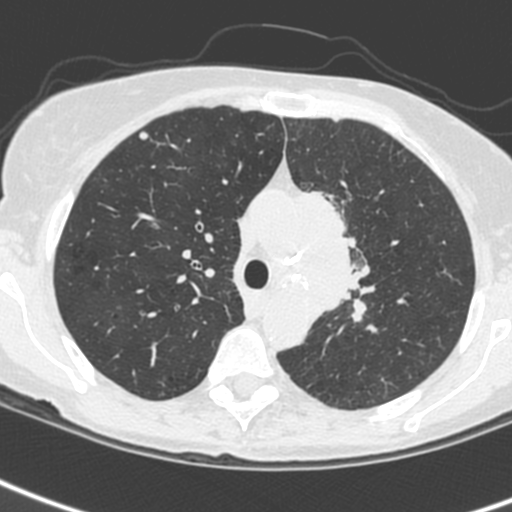
Low-dose screening chest CT, one axial slice. Slice 176 of 242 in the series (ordered by position). 120 kVp. Lung window (W 1500 / L -600 HU). 1.3 mm slice thickness. 512 × 512 image matrix.
Structures marked on this image (manually delineated by an expert):
- lesion 3 (tumor, upper lobe of left lung): bounding box [x1, y1, x2, y2] px = [302, 191, 357, 313]